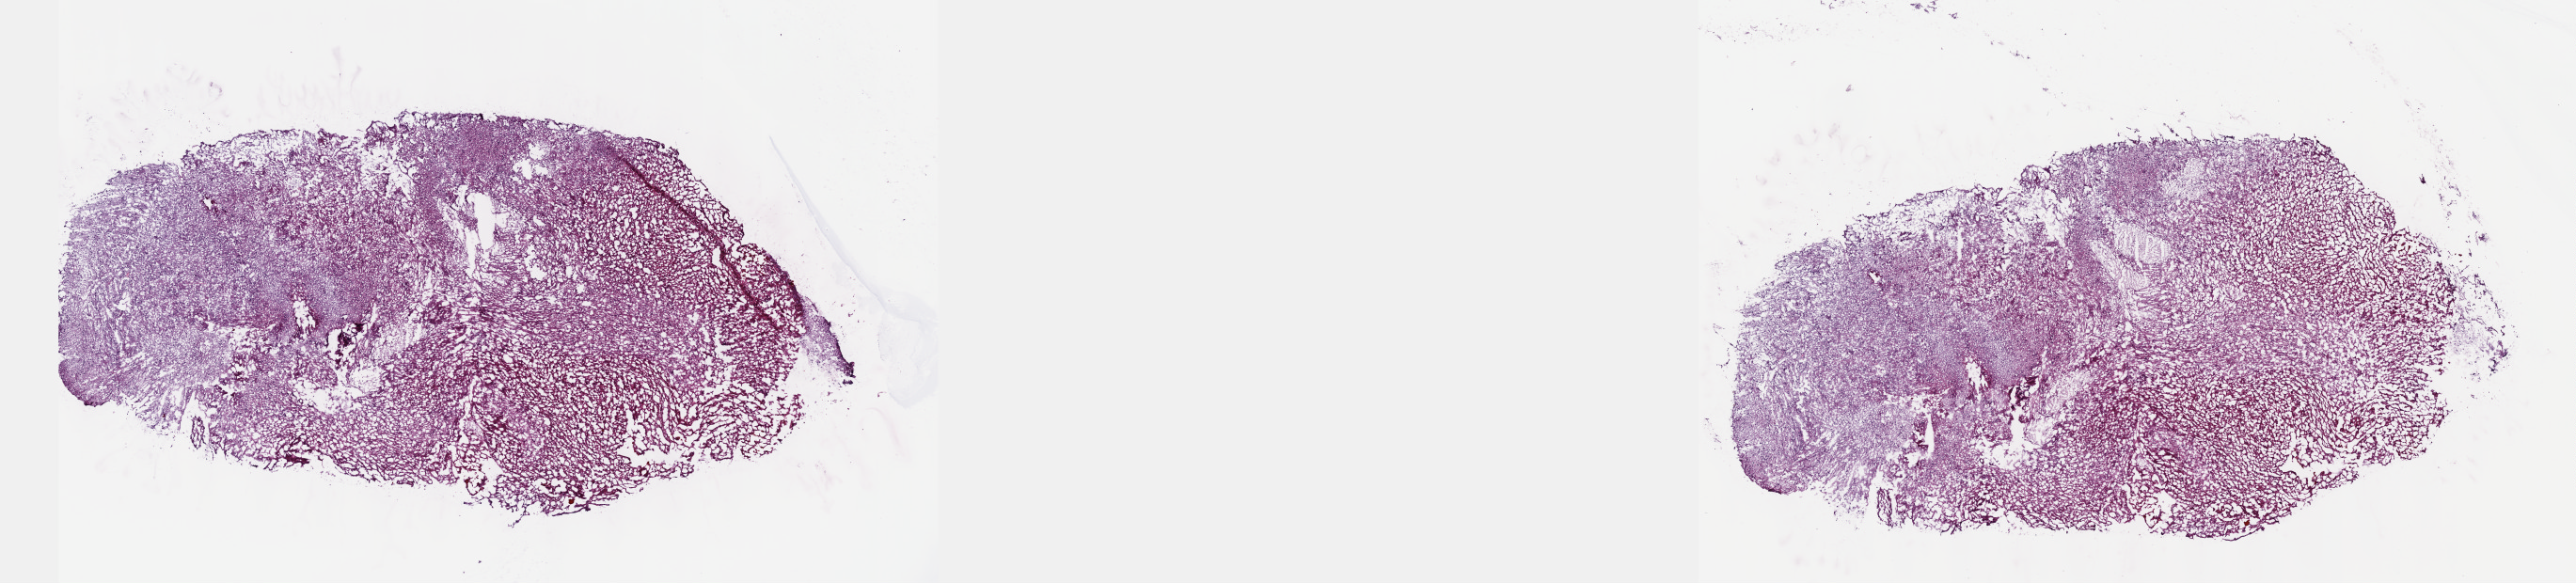
H&E-stained whole-slide image, low-resolution overview of the scanned area, about 22.1 x 5.0 mm; frozen section from the top of the tissue portion; sample: primary tumour, brain. Patient: male, age at initial diagnosis 32 years. Histologic grade: G2 (moderately differentiated). Slide review estimates, as recorded: tumour cells 40%, tumour nuclei 80%, normal cells 10%, stromal cells 50%, necrosis 0%. Infiltration values recorded for this section: lymphocyte infiltration 0%, monocyte infiltration 0%, neutrophil infiltration 0%.
Laterality: midline. Histologic diagnosis: Astrocytoma, NOS (cerebrum).